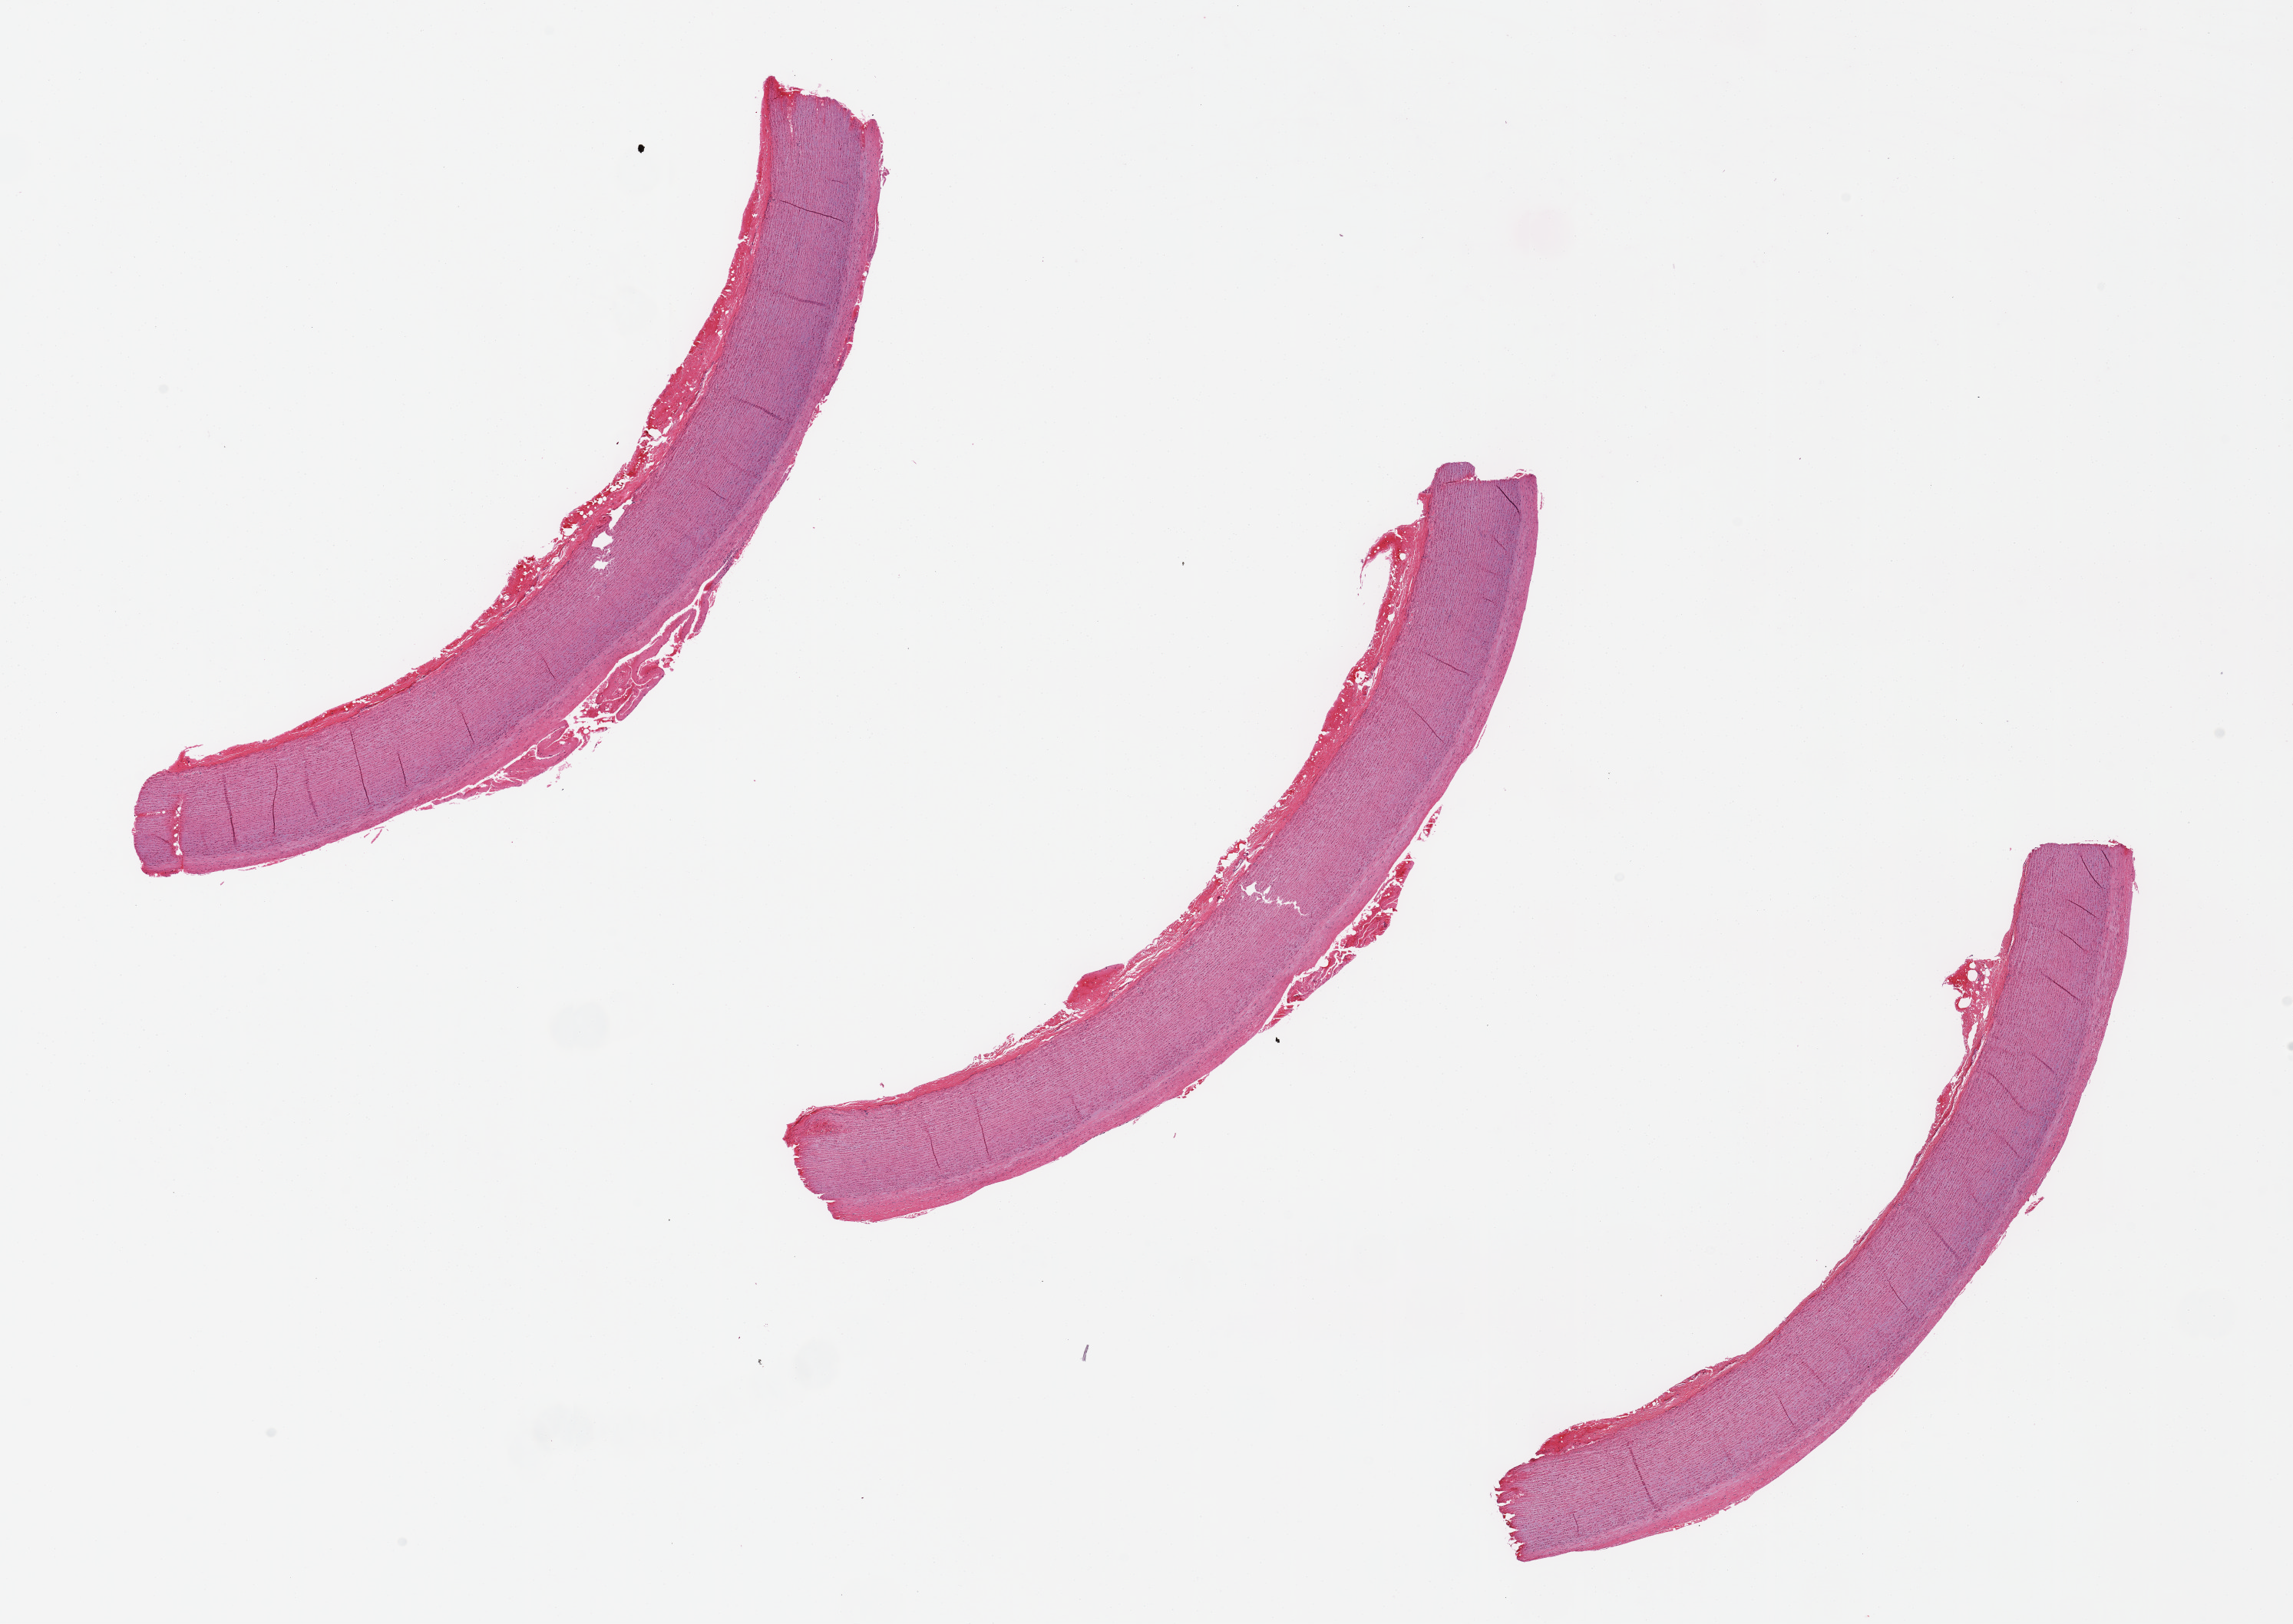
Digitized H&E-stained section, brightfield — low-resolution overview of the scanned area, about 23.6 x 16.7 mm. PAXgene-fixed, paraffin-embedded tissue. Section of aorta (target tissue). Tissue donor sample.
Pathologist's review note for this sample: 3 pieces.